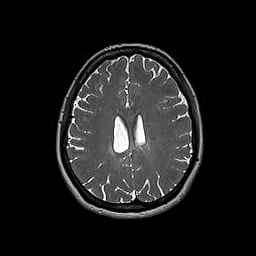
Brain MRI from a brain-tumour surgery series, one axial slice. Slice 73 of 192 in the series (ordered by position). 1 mm slice thickness. 256 × 256 image matrix. Case-level facts recorded for this patient, not image findings: histopathology: Oligodendroglioma; WHO grade: 2; IDH mutation: yes; tumour location: Right Parietal.
Structures marked on this image (outlined manually by an expert reader):
- tumour: bounding box (x1, y1, x2, y2) in pixels: (109, 146, 117, 155)